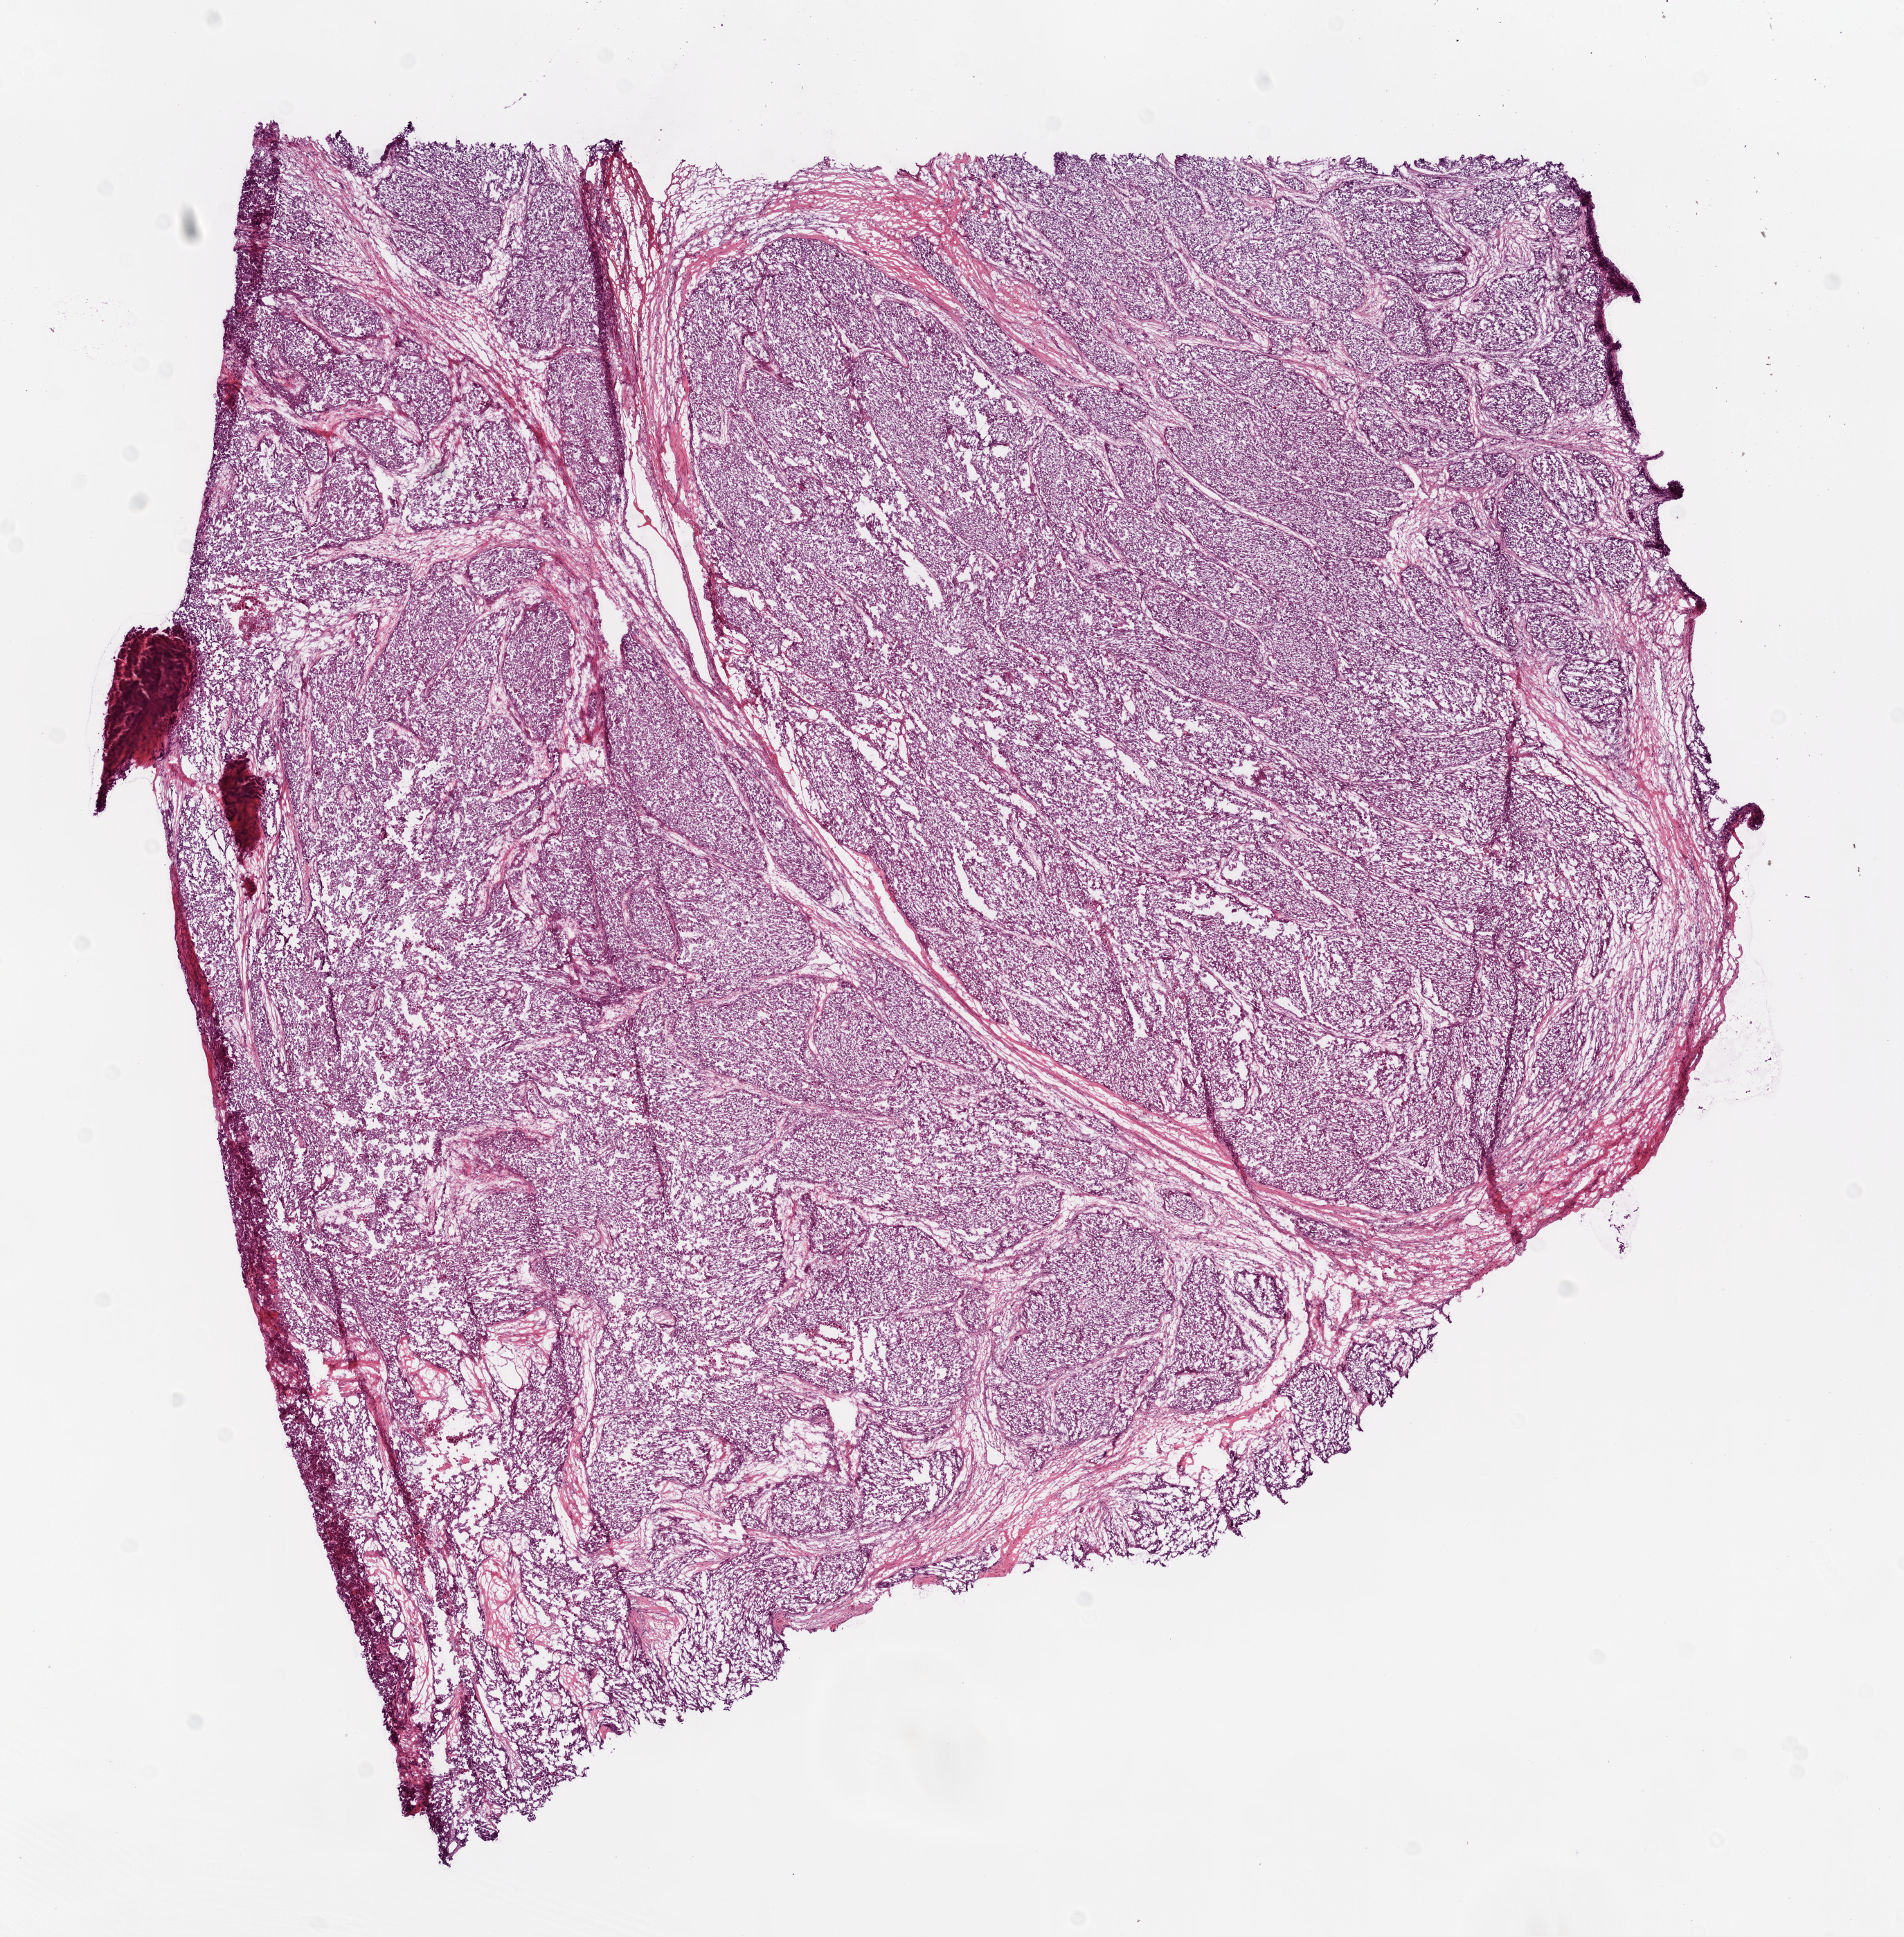
Hematoxylin and eosin (H&E) stained whole-slide image — a low-resolution overview of the entire scanned area, about 11.0 x 11.2 mm (slide scanned at 20x), frozen section from the bottom of the tissue portion, ovary, primary tumour sample. Female patient; age at initial diagnosis 79 years. Histologic grade: G3 (poorly differentiated). Slide review estimates, as recorded: tumour cells 90%, tumour nuclei 90%, normal cells 0%, stromal cells 10%, necrosis 0%. Infiltration values recorded for this section: lymphocyte infiltration 0%, monocyte infiltration 2%, neutrophil infiltration 0%.
Histologic diagnosis: Serous cystadenocarcinoma, NOS. Laterality: bilateral. FIGO stage: IIIC.